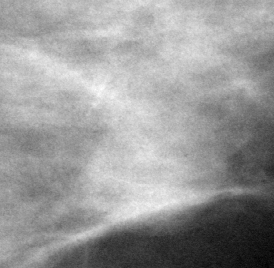
Crop from a digitized film mammogram around one marked abnormality; left breast; MLO view; BI-RADS breast density category 3 (scale 1–4).
- Finding: mass, shape oval, margins circumscribed; BI-RADS assessment category 4; pathology result (as recorded, not read from the image): benign.